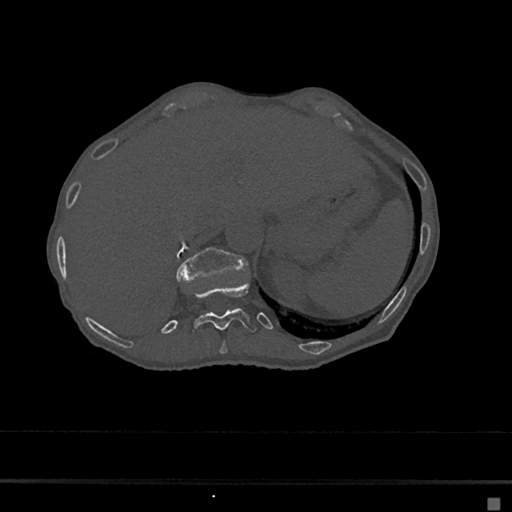
CT including the spine, one axial slice. Slice 167 of 797 in the series (ordered by position). 120 kVp. Bone window (W 1800 / L 400 HU). 512 × 512 image matrix. Patient: female, 68 years. Case-level facts recorded for this patient, not image findings: primary cancer: renal.
Structures marked on this image (semi-automatic segmentation, software-assisted and operator-edited):
- T10 vertebra: bounding box <220,341,228,355> (left, top, right, bottom; pixels)
- T11 vertebra: <192,281,257,335>
- T12 vertebra: <175,247,247,282>